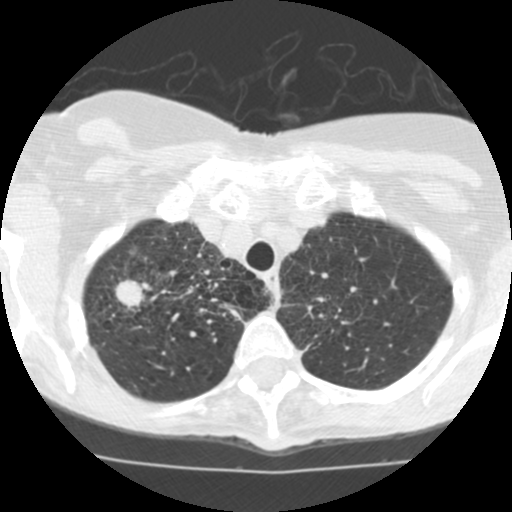
Low-dose screening chest CT, one axial slice. Slice 96 of 115 in the series (ordered by position). Reconstruction kernel STANDARD. 120 kVp. Lung window (W 1500 / L -600 HU). 512 × 512 image matrix, field of view 280 × 280 mm.
Outlined on this slice (outlined manually by an expert reader):
- lesion 1 (tumor, upper lobe of right lung): bounding box <115,280,143,310> (left, top, right, bottom; pixels)